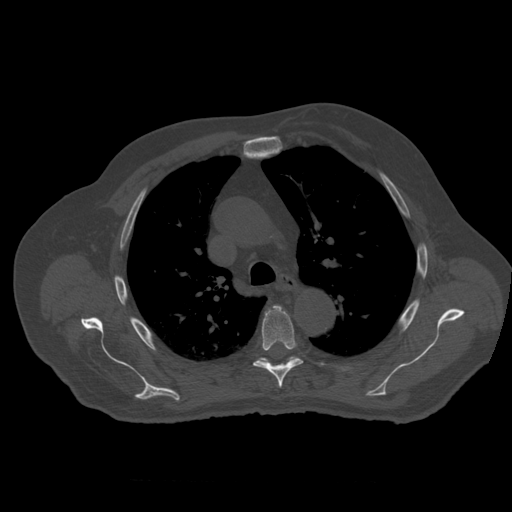
CT including the spine, one axial slice; slice 398 of 399 in the series (ordered by position); 120 kVp; bone window (W 1800 / L 400 HU); 1.25 mm slice thickness; 512 × 512 image matrix, field of view 407 × 407 mm. Patient age 73 years. From the clinical record (not read from this slice): primary cancer: prostate; vertebrae with lytic lesions (as recorded): L2.
Outlined on this slice (semi-automatic segmentation, software-assisted and operator-edited):
- T5 vertebra: bounding box <254,306,303,389> (left, top, right, bottom; pixels)
- T6 vertebra: <257,357,299,364>